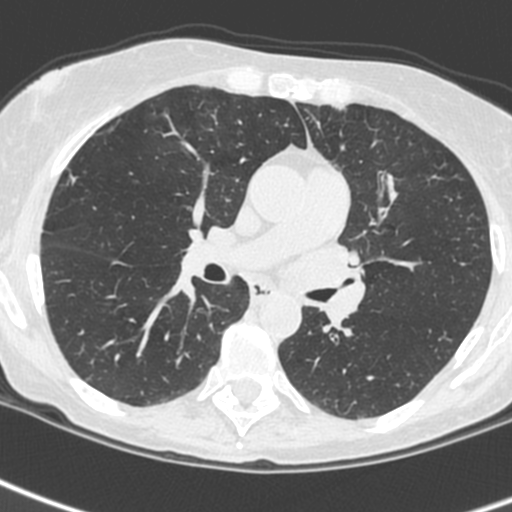
Low-dose screening chest CT, one axial slice. Slice 140 of 242 in the series (ordered by position). Lung window (W 1500 / L -600 HU). 512 × 512 image matrix, field of view 284 × 284 mm.
Structures marked on this image (expert manual segmentation):
- lesion 3 (tumor, upper lobe of left lung): bounding box <293,242,365,324> (left, top, right, bottom; pixels)